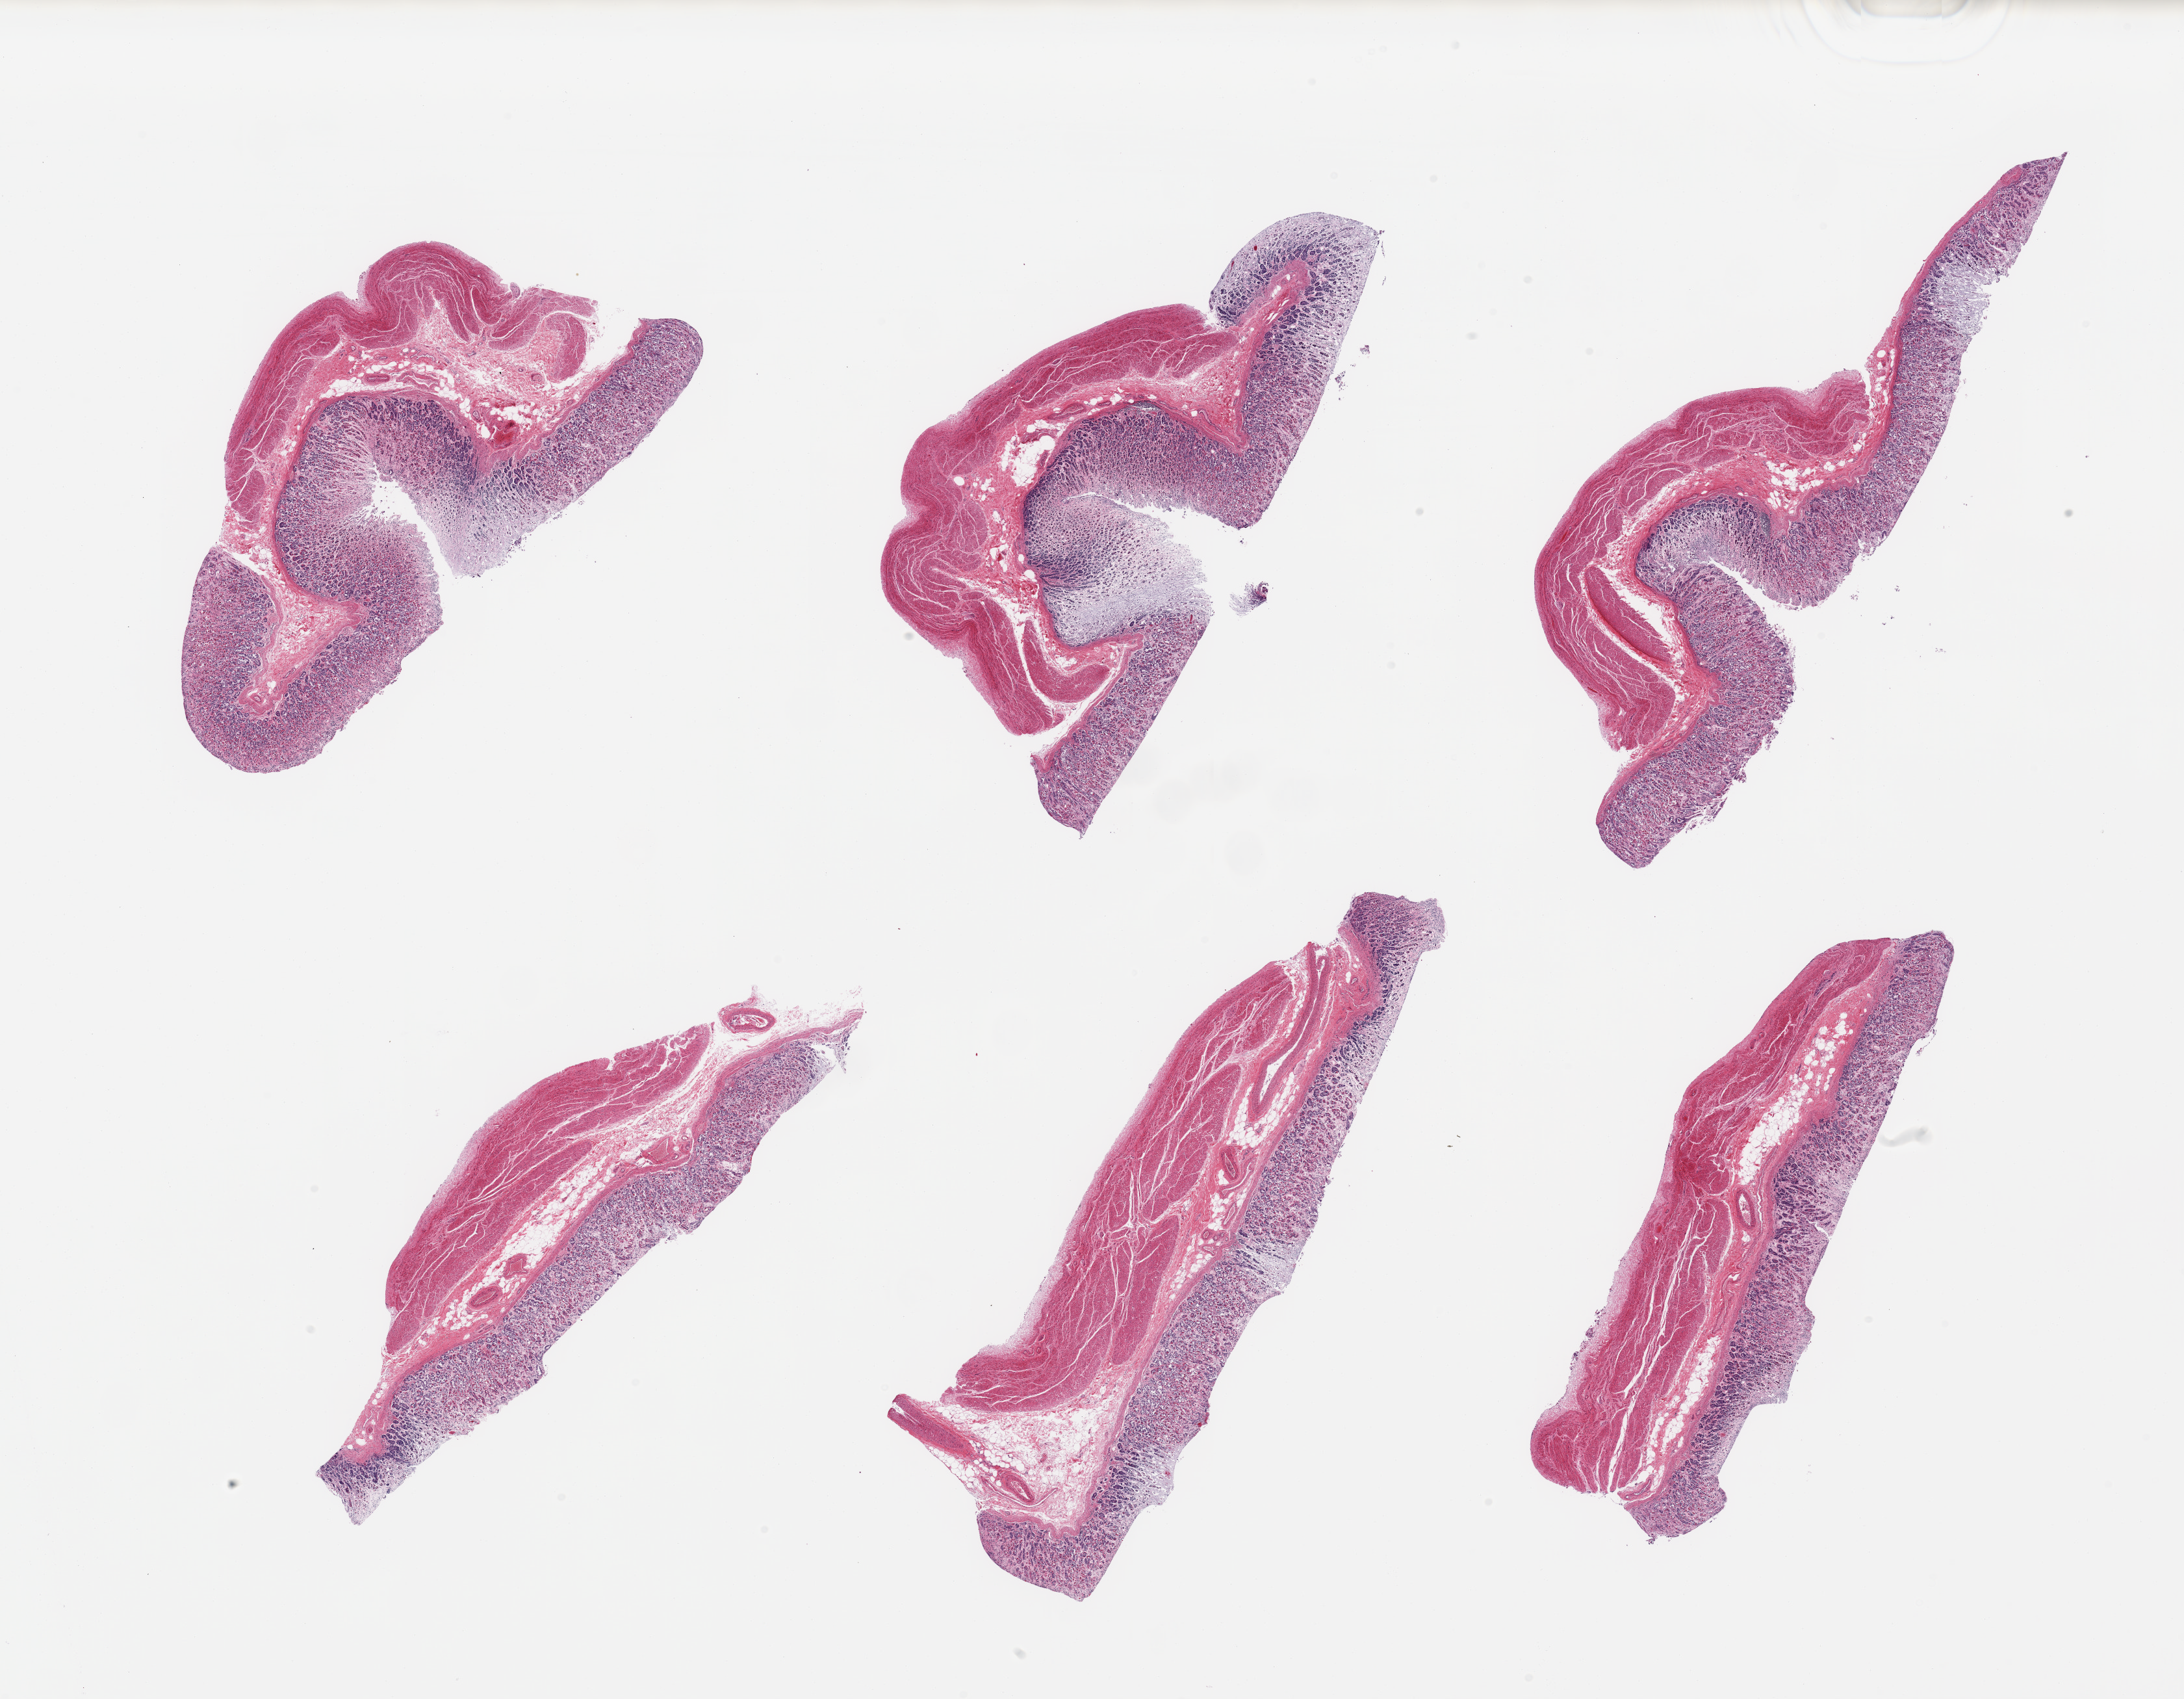
Haematoxylin and eosin whole-slide image — whole scanned area (about 26.6 x 20.7 mm) shown as a low-resolution overview; PAXgene-fixed paraffin-embedded (PFPE) section; section of stomach (target tissue); tissue donor sample. Donor: male.
Reviewer comment on this tissue sample: 6 pieces; mucosa largely autolyzed; muscularis intact.